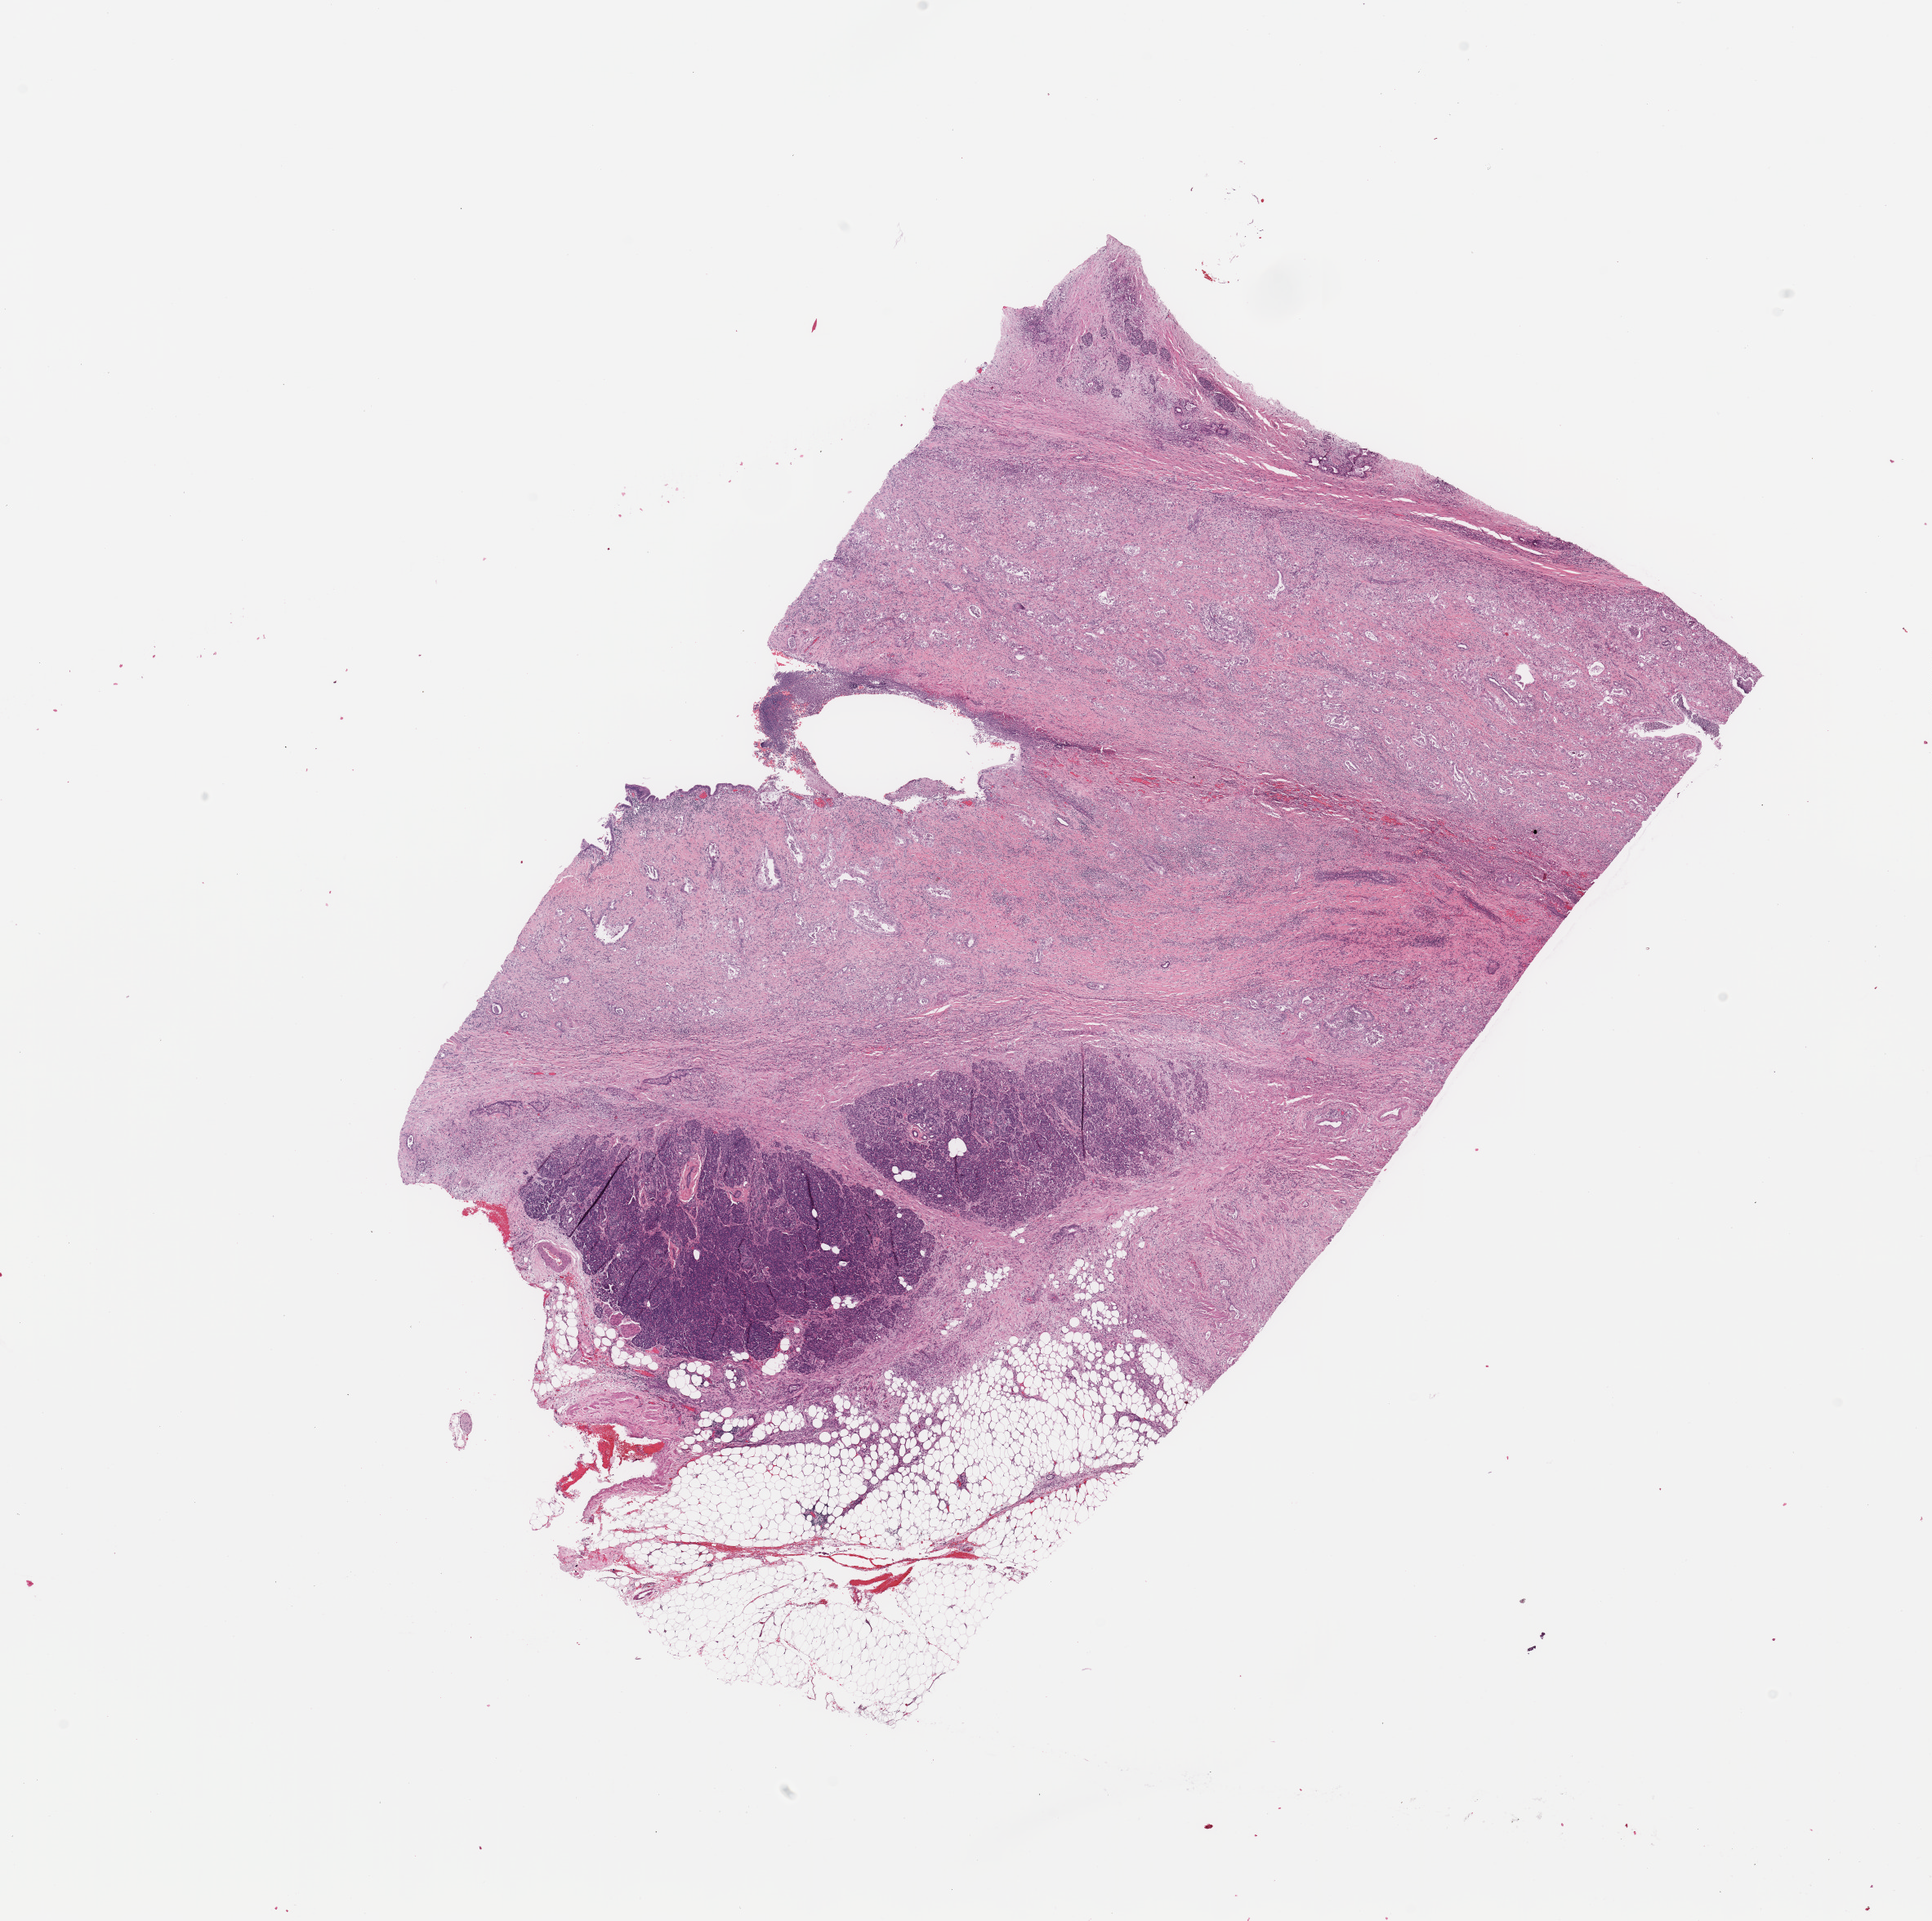
Digitized Hematoxylin and eosin (H&E) stained tissue section (whole slide), a low-resolution overview of the entire scanned area, about 18.7 x 18.6 mm (acquisition: 20x scan); pancreas, tumour tissue. Female, 64 y/o. Histologic grade: G2 (moderately differentiated).
• primary tumour site (as recorded): head
• histologic diagnosis: Infiltrating duct carcinoma, NOS
• AJCC pathologic stage: IIA